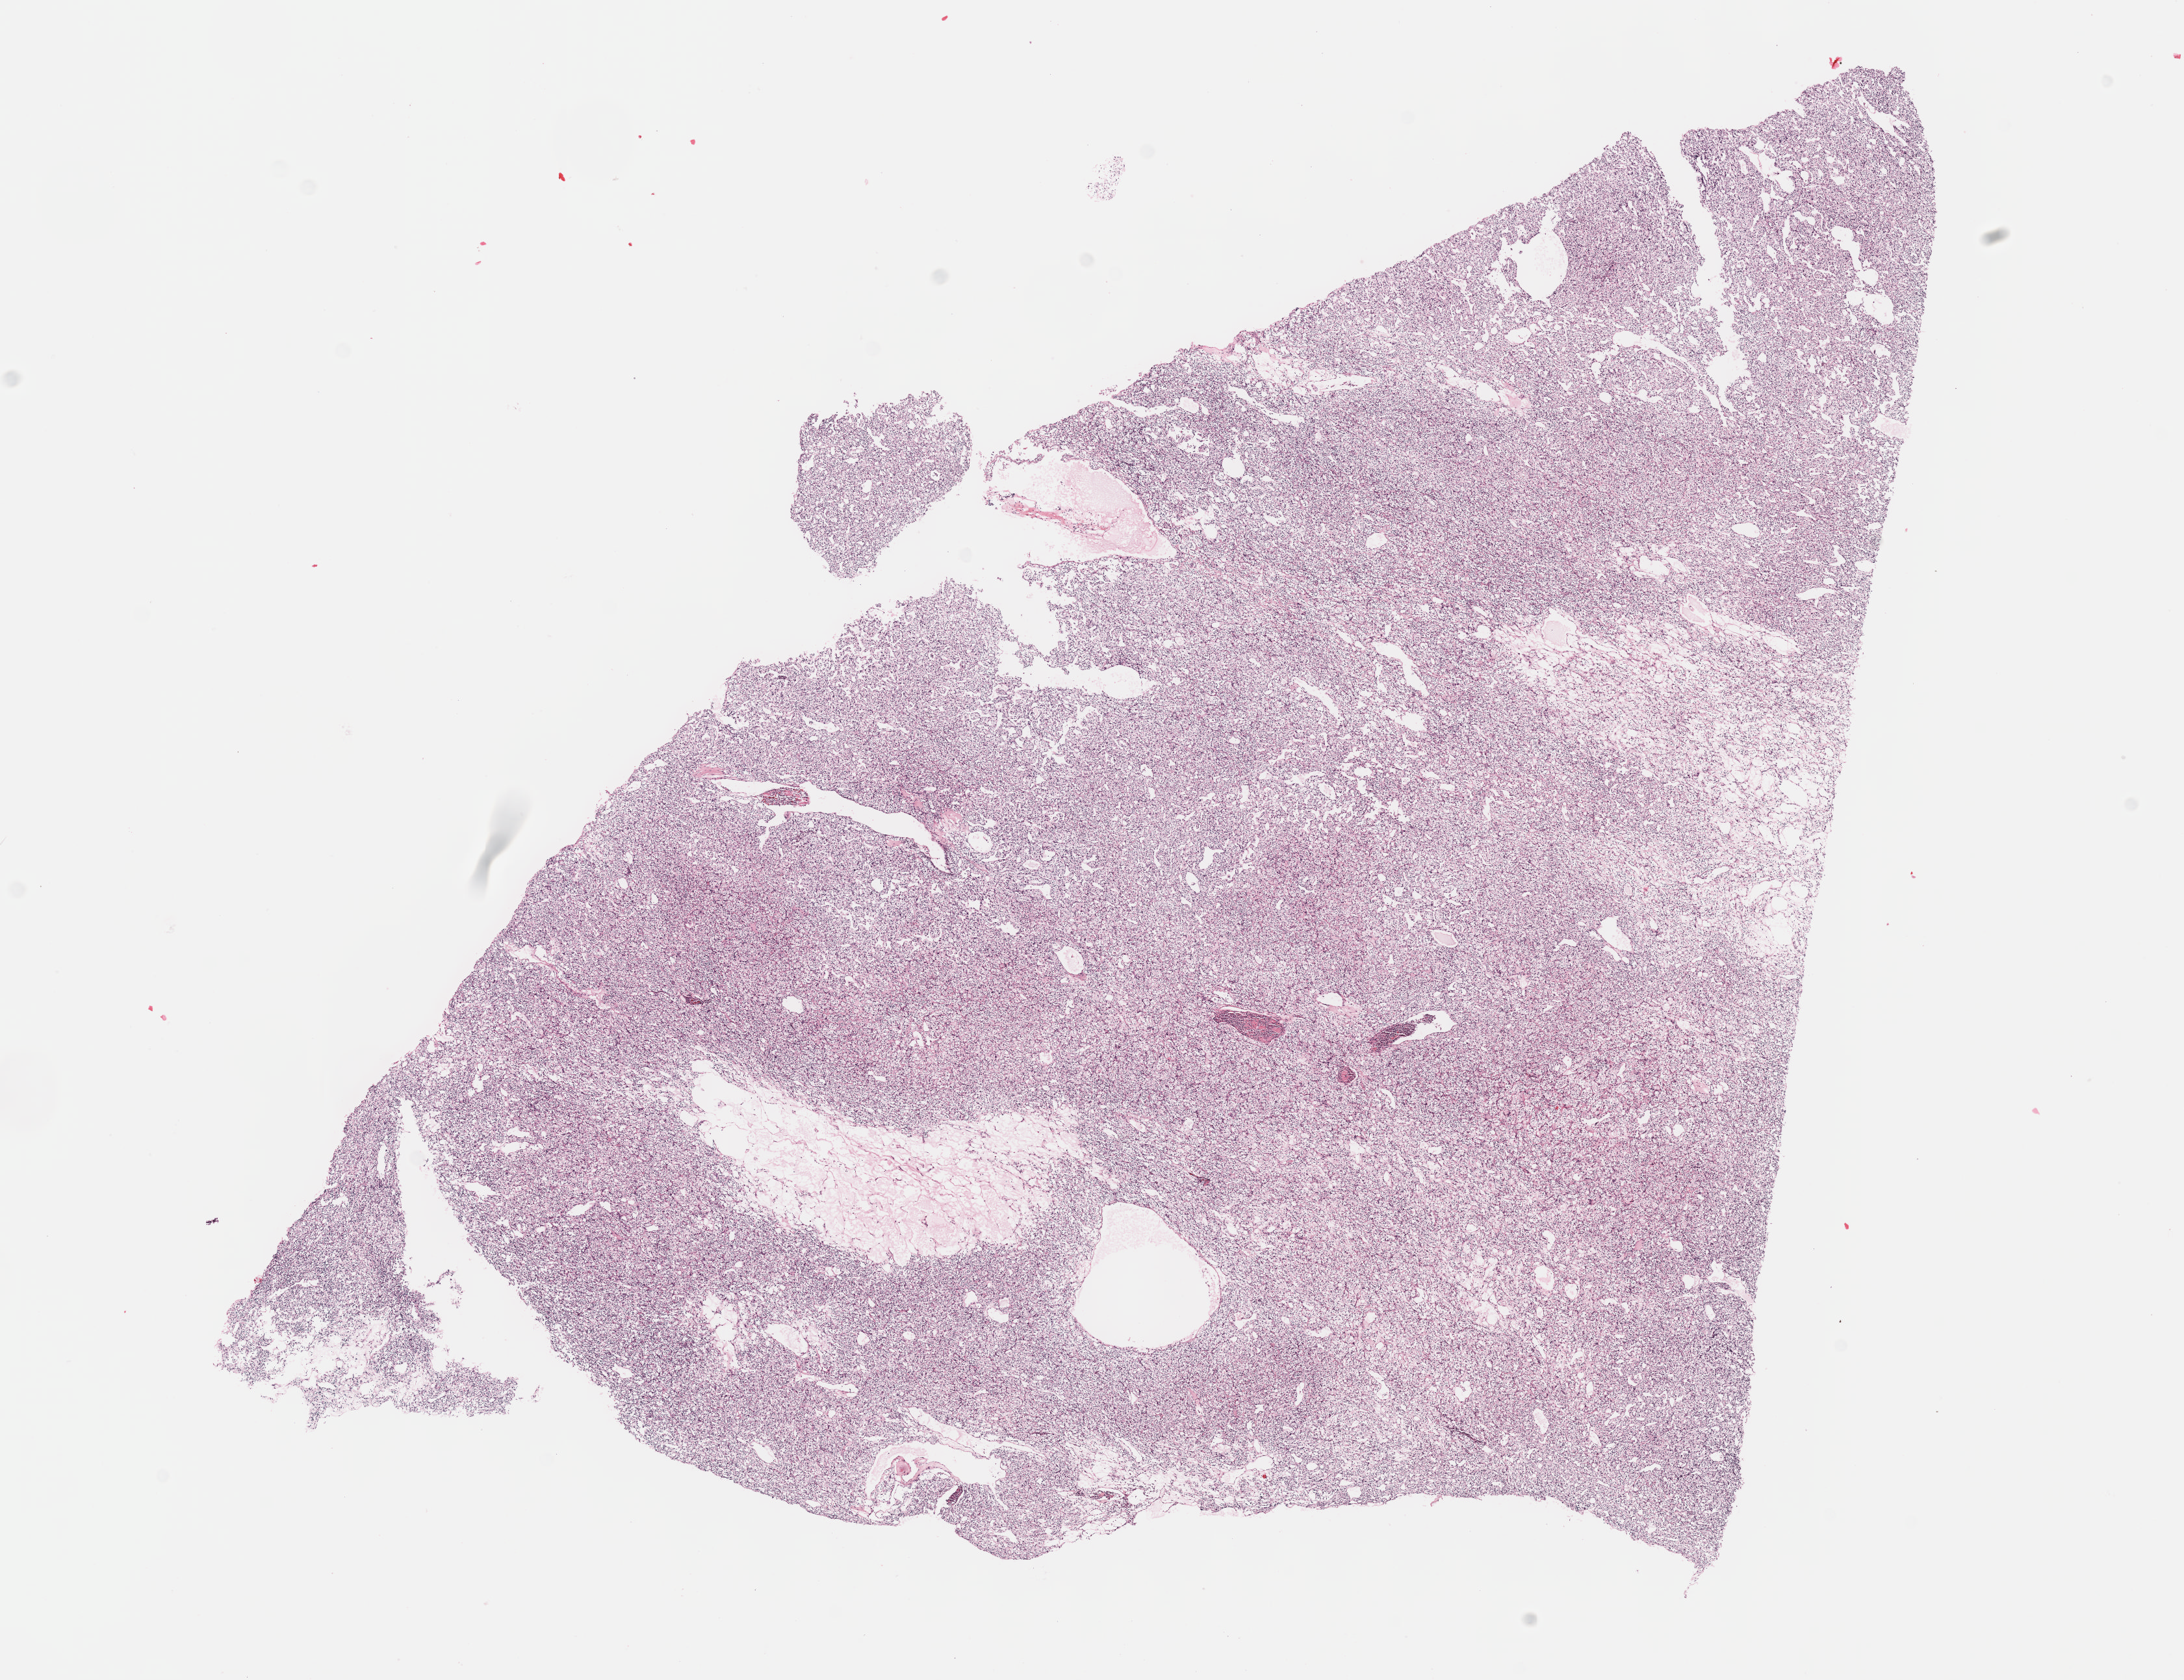
Digitized H&E tissue section (whole slide), shown as a low-resolution overview of the whole scanned area (about 13.6 x 10.5 mm), FFPE section, primary tumour sample from the kidney. Patient: male, age at initial diagnosis 62 years.
Pathologic diagnosis: Clear cell adenocarcinoma, NOS.